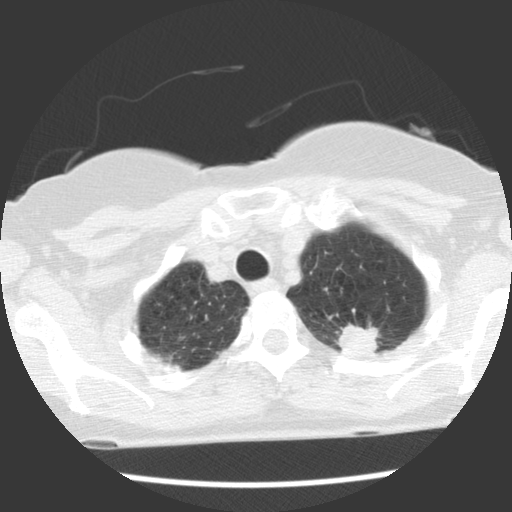
Low-dose screening chest CT, axial slice. Baseline screening round. Lung window (W 1500 / L -600 HU). 2.5 mm slice thickness. Standard (soft-tissue) reconstruction kernel (STANDARD). 512 × 512 image matrix. Female, age 66 years at enrolment. Former smoker at enrolment.
• Expert reader's lesion annotation, bounding box <318,305,387,365> (left, top, right, bottom; pixels).
• Reader record for this screening exam (exam-level; its link to the box is not recorded): non-calcified nodule or mass ≥4 mm, left upper lobe, 22 × 17 mm, spiculated (stellate) margins, soft tissue attenuation.
• Official screen result: positive, change unspecified: nodule(s) >= 4 mm or enlarging nodule(s), mass(es), or other non-specific abnormalities suspicious for lung cancer.
• Later outcome: lung cancer diagnosed 50 days after this screen — adenocarcinoma, NOS, left upper lobe, poorly differentiated (G3), stage IB (AJCC 6th edition), 40 mm at pathology.